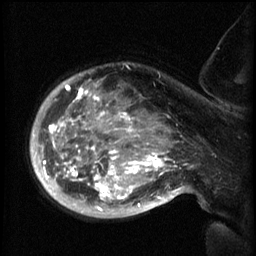
Breast MRI (dynamic contrast-enhanced), one sagittal slice; slice 46 of 60 in the series (ordered by position); 3 images stored at this slice position (order not interpretable as contrast timing); 1.5 T; TE 4.2 ms, TR 8.2 ms; 2.3 mm slice thickness; 256 × 256 image matrix. Patient: female, 50 years.
Outlined on this slice (semi-automatically segmented with operator editing):
- analysis volume of interest (the breast-tissue region the enhancement analysis was run in; not a lesion): bounding box [x1, y1, x2, y2] px = [50, 68, 169, 217]
- tumour enhancement mask (voxels above the 70 % enhancement threshold inside the analysis volume of interest): [50, 84, 169, 211]